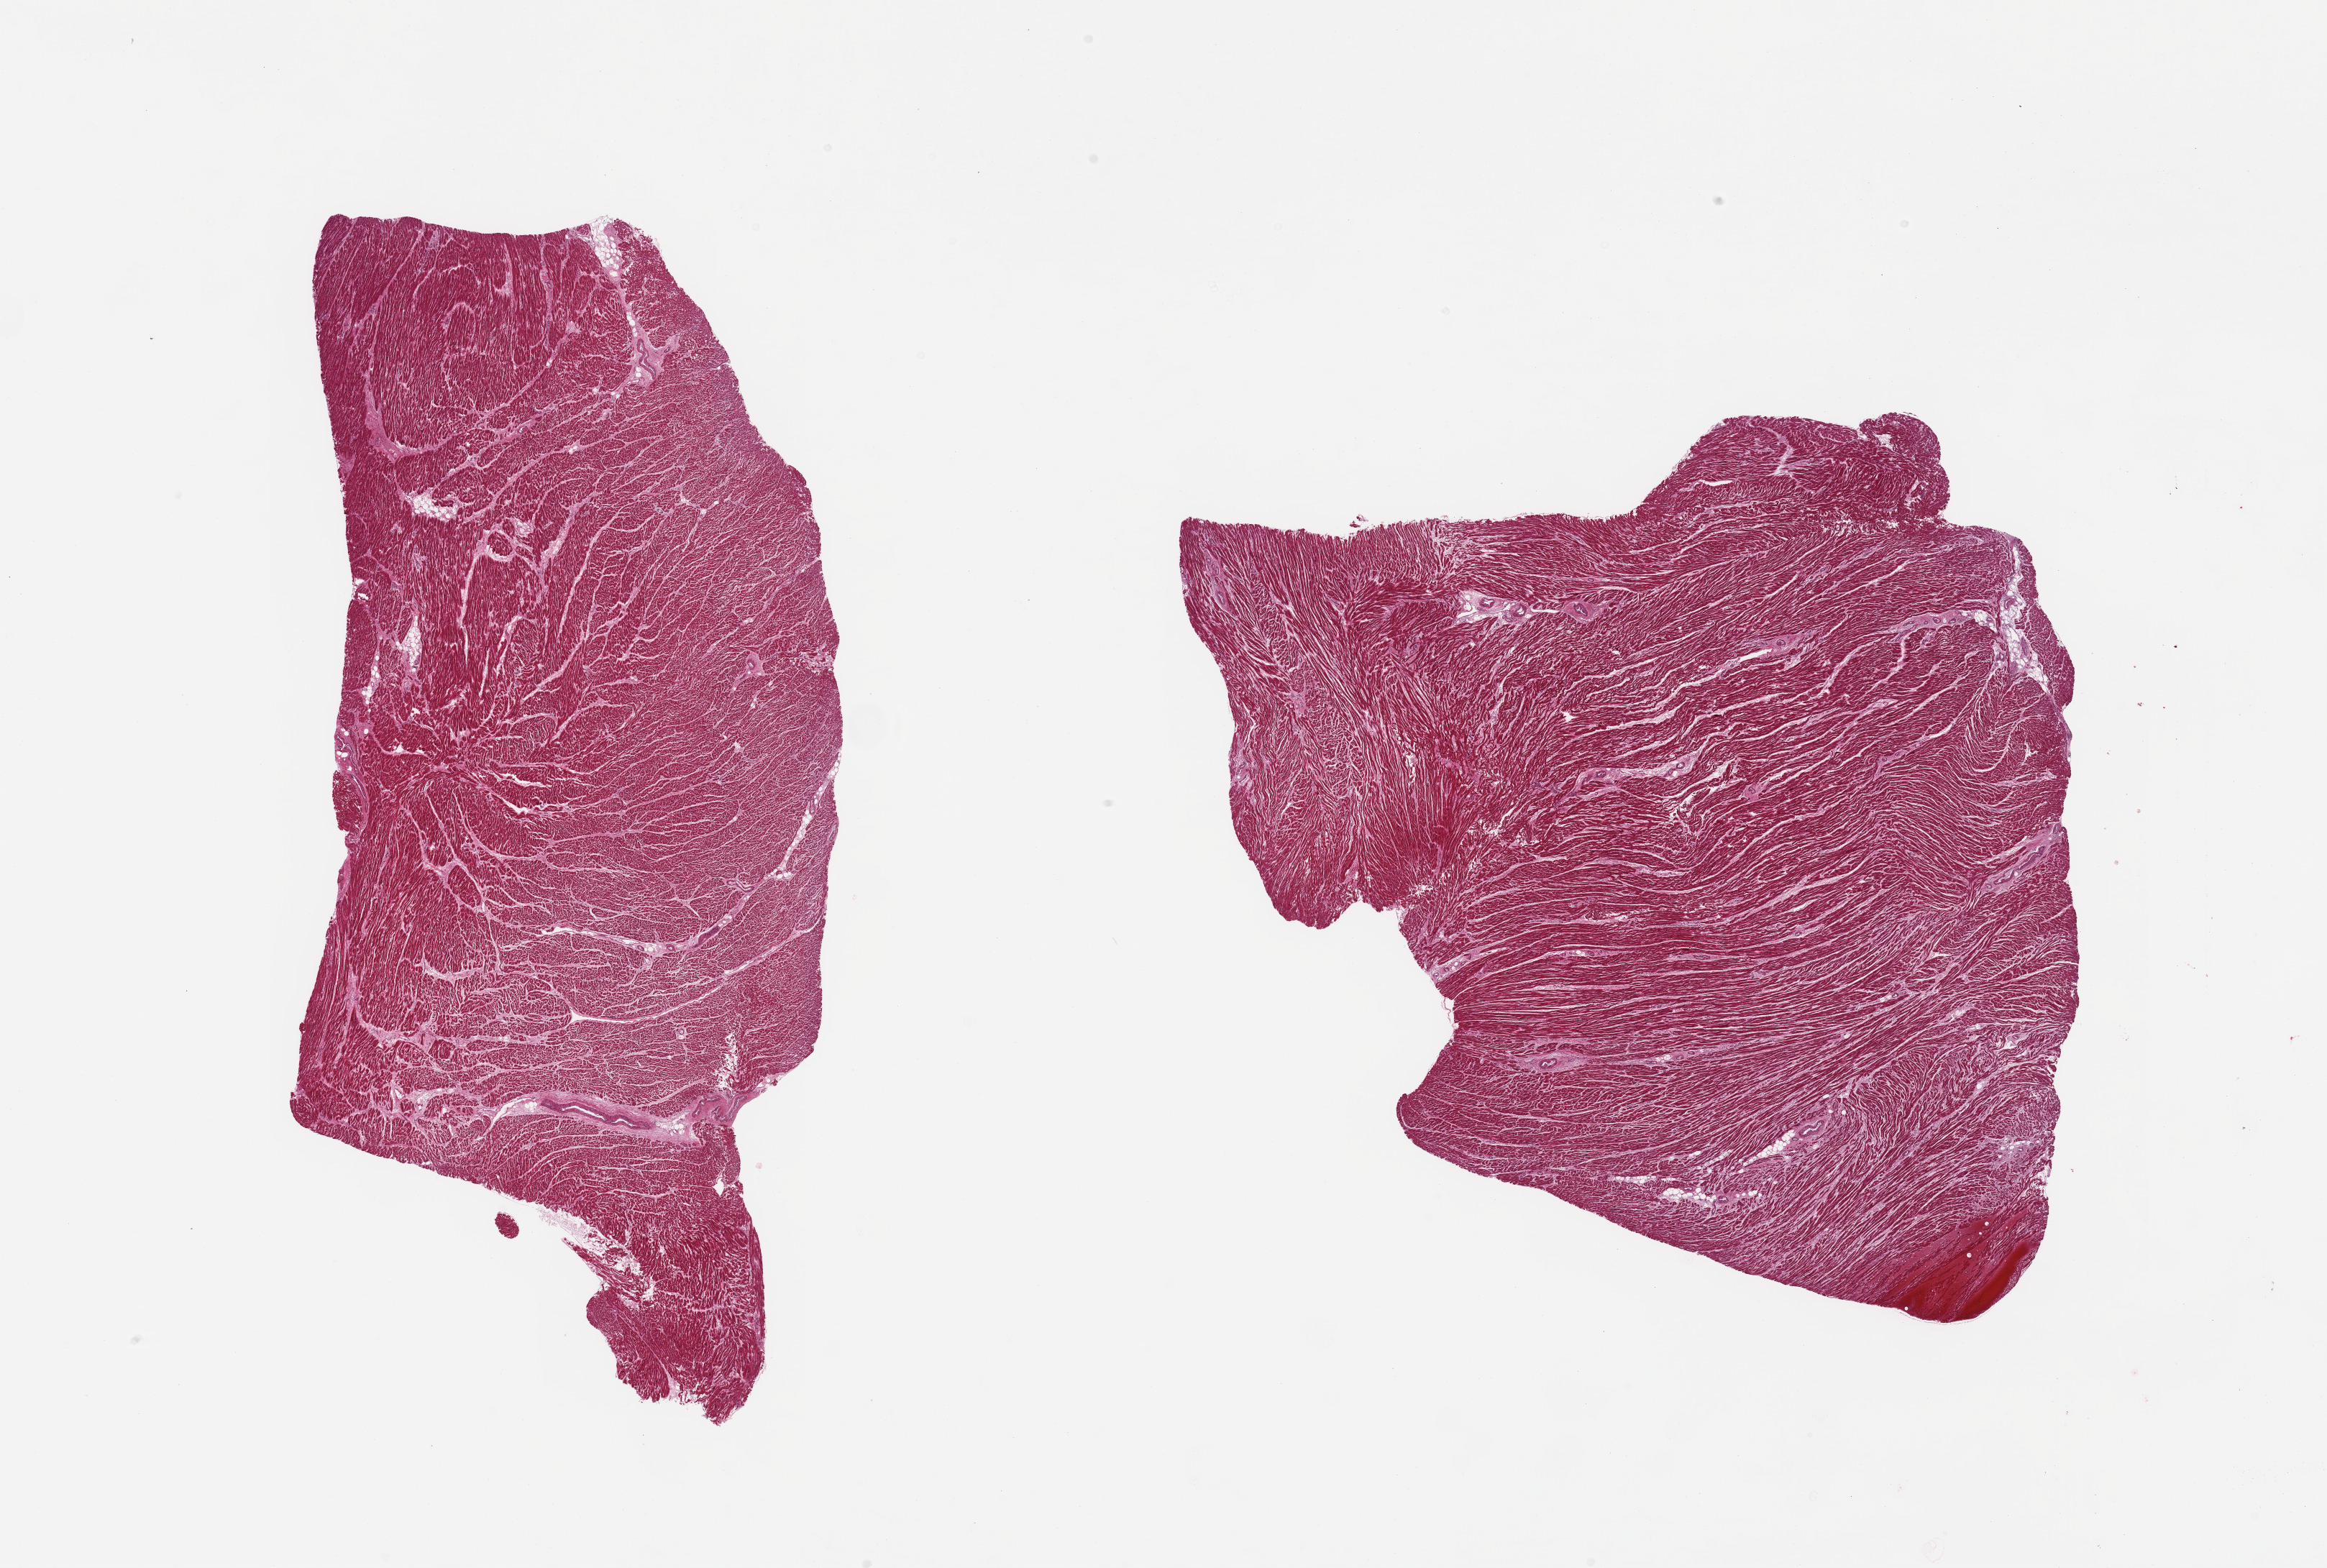
Digitized hematoxylin and eosin (H&E)-stained section, brightfield, whole scanned area (about 25.6 x 17.3 mm, from a 20x scan) shown as a low-resolution overview. PAXgene-fixed, paraffin-embedded tissue. Section of heart (target tissue). Donor tissue sample. Donor sex: male.
- reviewer comment on this tissue sample: 2 pieces; 1x2mm focal hemorrhage at 1 corner